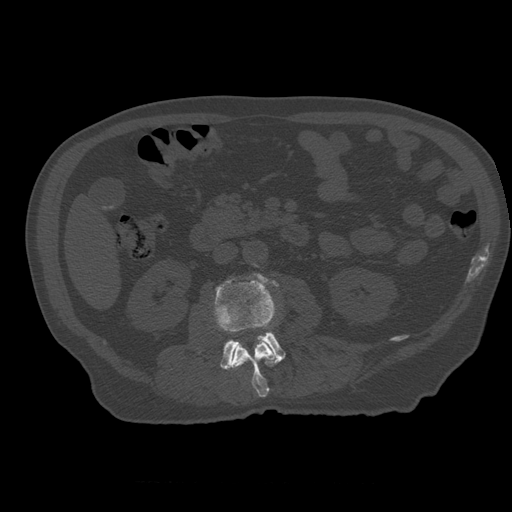
CT including the spine, one axial slice; position 200 of 399 along the scan axis; reconstruction kernel STANDARD; 120 kVp; bone window (W 1800 / L 400 HU); 1.25 mm slice thickness; 512 × 512 image matrix, field of view 407 × 407 mm. Patient age 73 years. From the clinical record (not read from this slice): primary cancer: prostate.
Annotated regions visible in this slice (semi-automatic segmentation, software-assisted and operator-edited):
- L2 vertebra: bounding box <231,340,276,398> (left, top, right, bottom; pixels)
- L3 vertebra: <215,273,286,370>